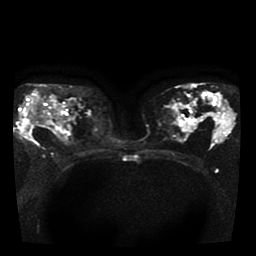
Breast MRI, one axial slice. Slice 23 of 41 in the series (ordered by position). Diffusion-weighted series; image 2 of 4 stored at this slice position (different b-values; order by instance number). 1.5 T. 5 mm slice thickness. 256 × 256 image matrix. Female patient.
Outlined on this slice (manually delineated by an expert):
- tumour on diffusion-weighted imaging: box from (x=21, y=96) to (x=36, y=140) px